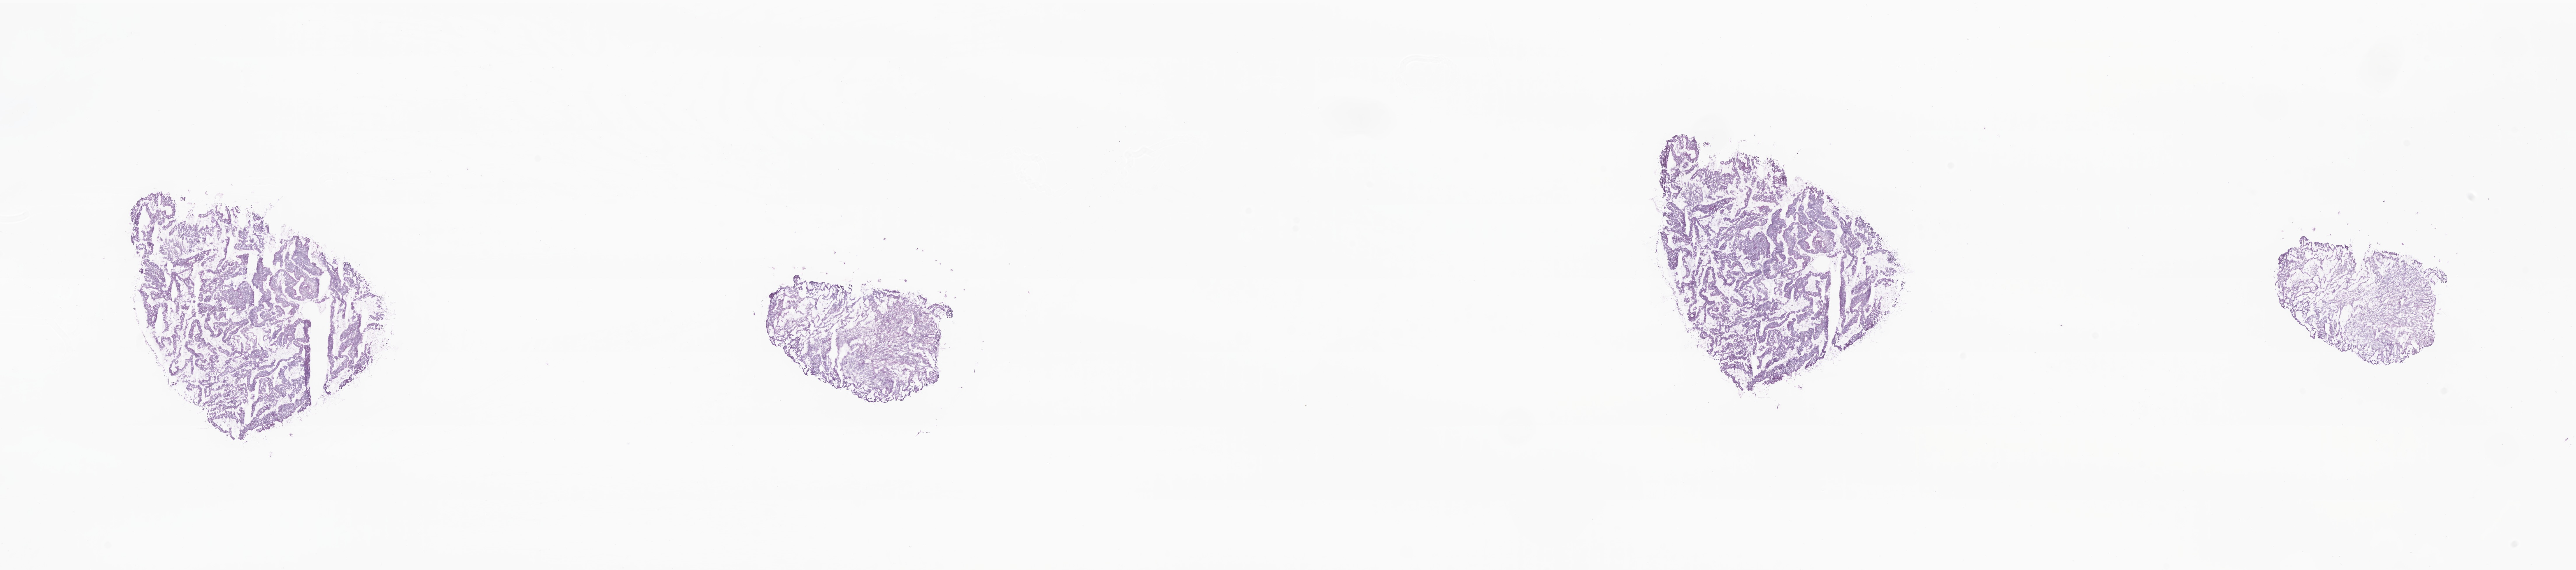
Digitized H&E-stained section, a low-resolution overview of the entire scanned area, about 37.3 x 8.2 mm. Cryosection. Primary tumor. Anatomic site: sigmoid colon. Male, age 66 years at initial diagnosis. Composition of this section per pathologist review: tumor cells 80%, tumor nuclei 80%, stromal cells 20%, necrosis 0%, normal cells 0%. Infiltration values recorded for this section: lymphocyte infiltration 4%, monocyte infiltration 2%, neutrophil infiltration 6%.
- histologic diagnosis: Adenocarcinoma, NOS